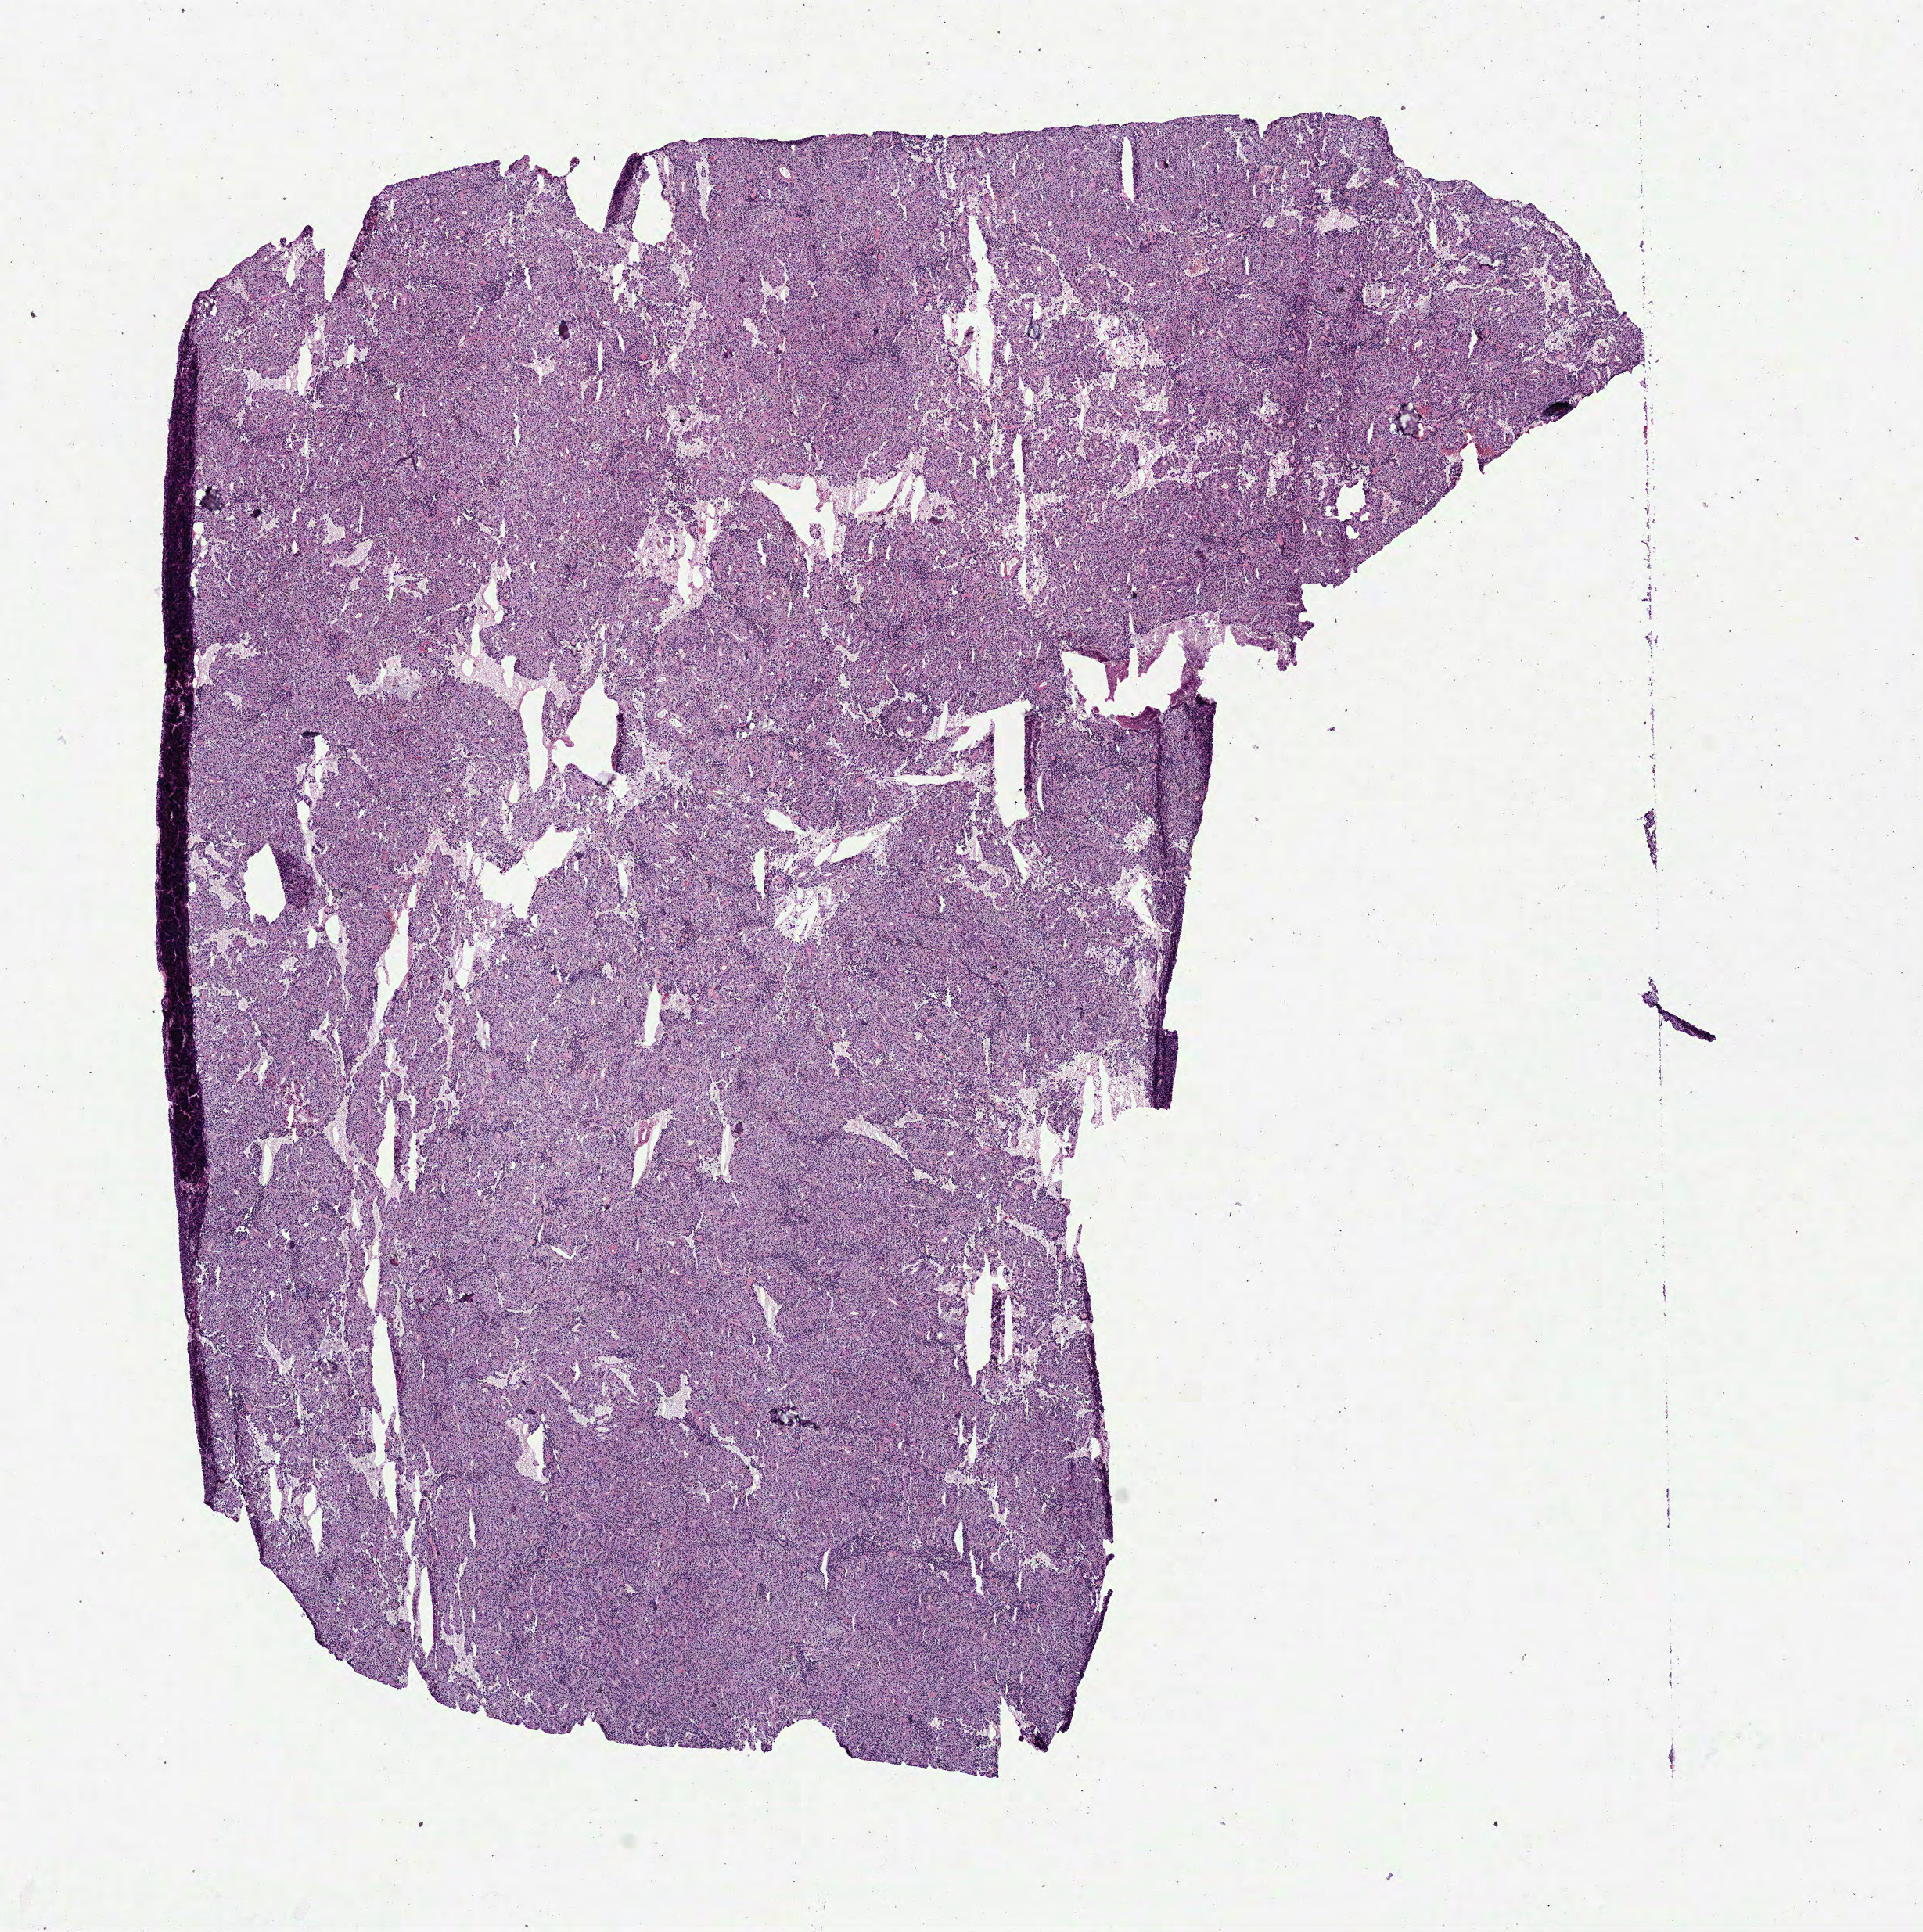
Digitized H&E tissue section (whole slide), shown as a low-resolution overview of the whole scanned area (about 9.9 x 10.0 mm, slide scanned at 40x); frozen section; kidney, primary tumour sample. Male, age 58 years at initial diagnosis. Slide review estimates, as recorded: tumour cells 95%, tumour nuclei 85%, normal cells 0%, stromal cells 5%, necrosis 0%.
- laterality: left
- diagnosis: Papillary adenocarcinoma, NOS
- AJCC pathologic stage: I